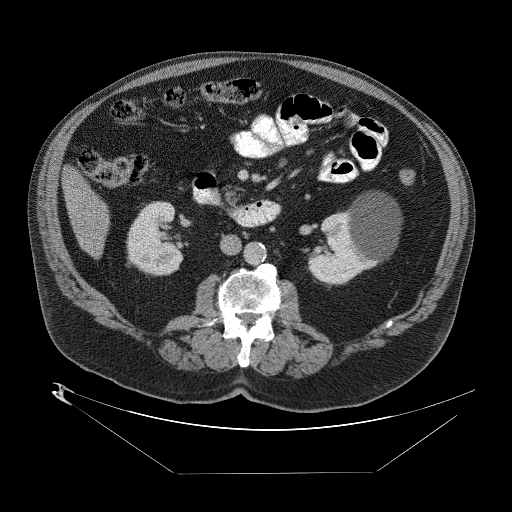
Contrast-enhanced abdominal CT (liver protocol), one axial slice; slice 11 of 89 in the series (ordered by position); reconstruction kernel STANDARD; 140 kVp; one of 2 acquisitions stored at this slice position; soft-tissue window (W 400 / L 40 HU); 2.5 mm slice thickness; 512 × 512 image matrix. Case-level facts recorded for this patient, not image findings: diagnosis: hepatocellular carcinoma (patient treated with transarterial chemoembolisation; whether this scan precedes or follows treatment is not stated here); TNM stage (as recorded): Stage-II; Child-Pugh class: B; tumour nodularity: multinodular; tumour size: 4 cm.
Annotated regions visible in this slice (semi-automatic segmentation, software-assisted and operator-edited):
- abdominal aorta: box from (x=244, y=242) to (x=266, y=266) px
- liver parenchyma outside the tumour (the mass and vessels are separate outlines, so this box may not span the whole liver): (x=62, y=162)–(x=110, y=256)
- liver vessels: (x=68, y=189)–(x=82, y=198)